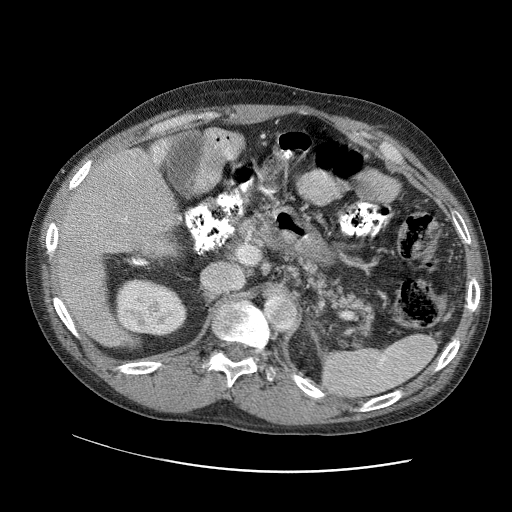
Contrast-enhanced abdominal CT (liver protocol), one axial slice; slice 61 of 109 in the series (ordered by position); reconstruction kernel STANDARD; 120 kVp; soft-tissue window (W 400 / L 40 HU); 2.5 mm slice thickness; 512 × 512 image matrix, field of view 400 × 400 mm. From the clinical record (not read from this slice): diagnosis: hepatocellular carcinoma (patient treated with transarterial chemoembolisation; whether this scan precedes or follows treatment is not stated here); TNM stage (as recorded): Stage-IIIC; Child-Pugh class: B; tumour nodularity: uninodular.
Annotated regions visible in this slice (semi-automatically segmented with operator editing):
- liver parenchyma outside the tumour (the mass and vessels are separate outlines, so this box may not span the whole liver): box from (x=54, y=138) to (x=180, y=334) px
- liver vessels: (x=73, y=139)–(x=165, y=292)